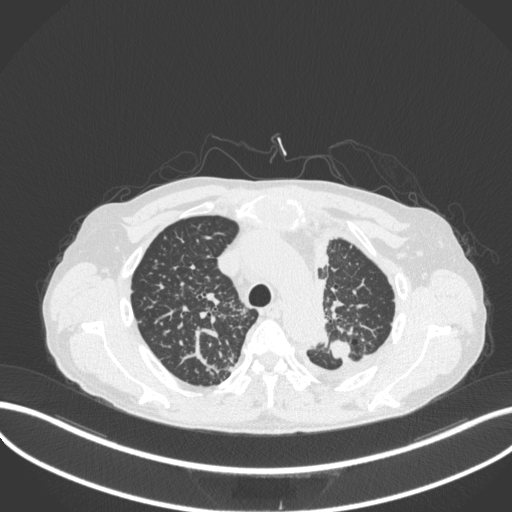
Chest CT, one axial slice. Slice 270 of 319 in the series (ordered by position). Lung window (W 1500 / L -600 HU). 1 mm slice thickness. 512 × 512 image matrix. Patient: male, 58 years. Case-level facts recorded for this patient, not image findings: clinical TNM (as recorded): T1c N3 M1.
Structures marked on this image (bounding box drawn by a radiologist):
- lung tumour (recorded histology: adenocarcinoma): bounding box <326,337,353,362> (left, top, right, bottom; pixels)